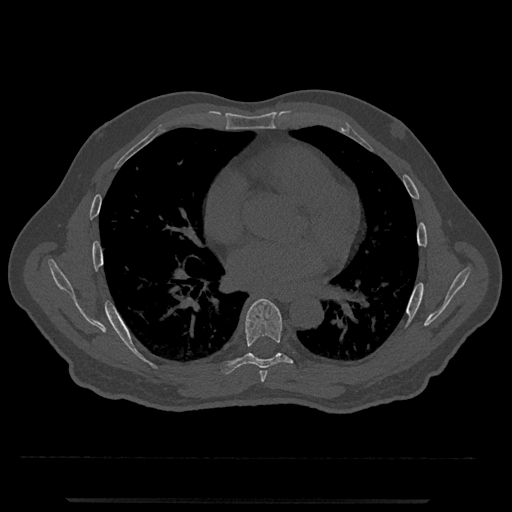
CT including the spine, one axial slice; position 686 of 797 along the scan axis; bone window (W 1800 / L 400 HU); 0.5 mm slice thickness; 512 × 512 image matrix, field of view 419 × 419 mm. Male patient, age 63 years. Case-level facts recorded for this patient, not image findings: primary cancer: prostate.
Structures marked on this image (semi-automatically segmented with operator editing):
- T6 vertebra: bounding box [x1, y1, x2, y2] px = [259, 371, 267, 383]
- T7 vertebra: [220, 299, 293, 375]